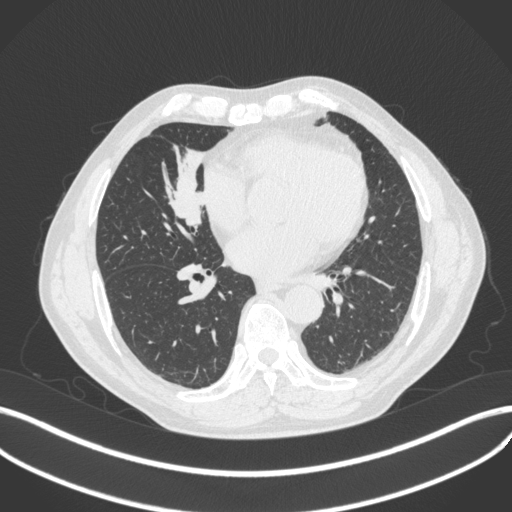
Chest CT, one axial slice; position 171 of 429 along the scan axis; lung window (W 1500 / L -600 HU); 1 mm slice thickness; 512 × 512 image matrix, field of view 400 × 400 mm. Male patient, age 61 years. From the clinical record (not read from this slice): clinical TNM (as recorded): T2b N1 M0.
Annotated regions visible in this slice (bounding box drawn by a radiologist):
- lung tumour (recorded histology: squamous cell carcinoma): bounding box <154,146,212,235> (left, top, right, bottom; pixels)